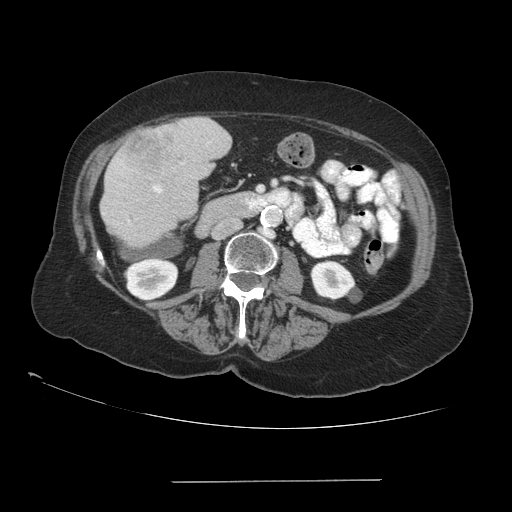
Contrast-enhanced abdominal CT (liver protocol), one axial slice. Slice 28 of 89 in the series (ordered by position). Soft-tissue window (W 400 / L 40 HU). 2.5 mm slice thickness. 512 × 512 image matrix, field of view 400 × 400 mm. Case-level facts recorded for this patient, not image findings: diagnosis: hepatocellular carcinoma (patient treated with transarterial chemoembolisation; whether this scan precedes or follows treatment is not stated here); TNM stage (as recorded): Stage-IVA; Child-Pugh class: A.
Structures marked on this image (semi-automatic segmentation, software-assisted and operator-edited):
- liver parenchyma outside the tumour (the mass and vessels are separate outlines, so this box may not span the whole liver): bounding box <100,118,230,246> (left, top, right, bottom; pixels)
- mass: <124,125,174,170>
- liver vessels: <153,186,162,193>